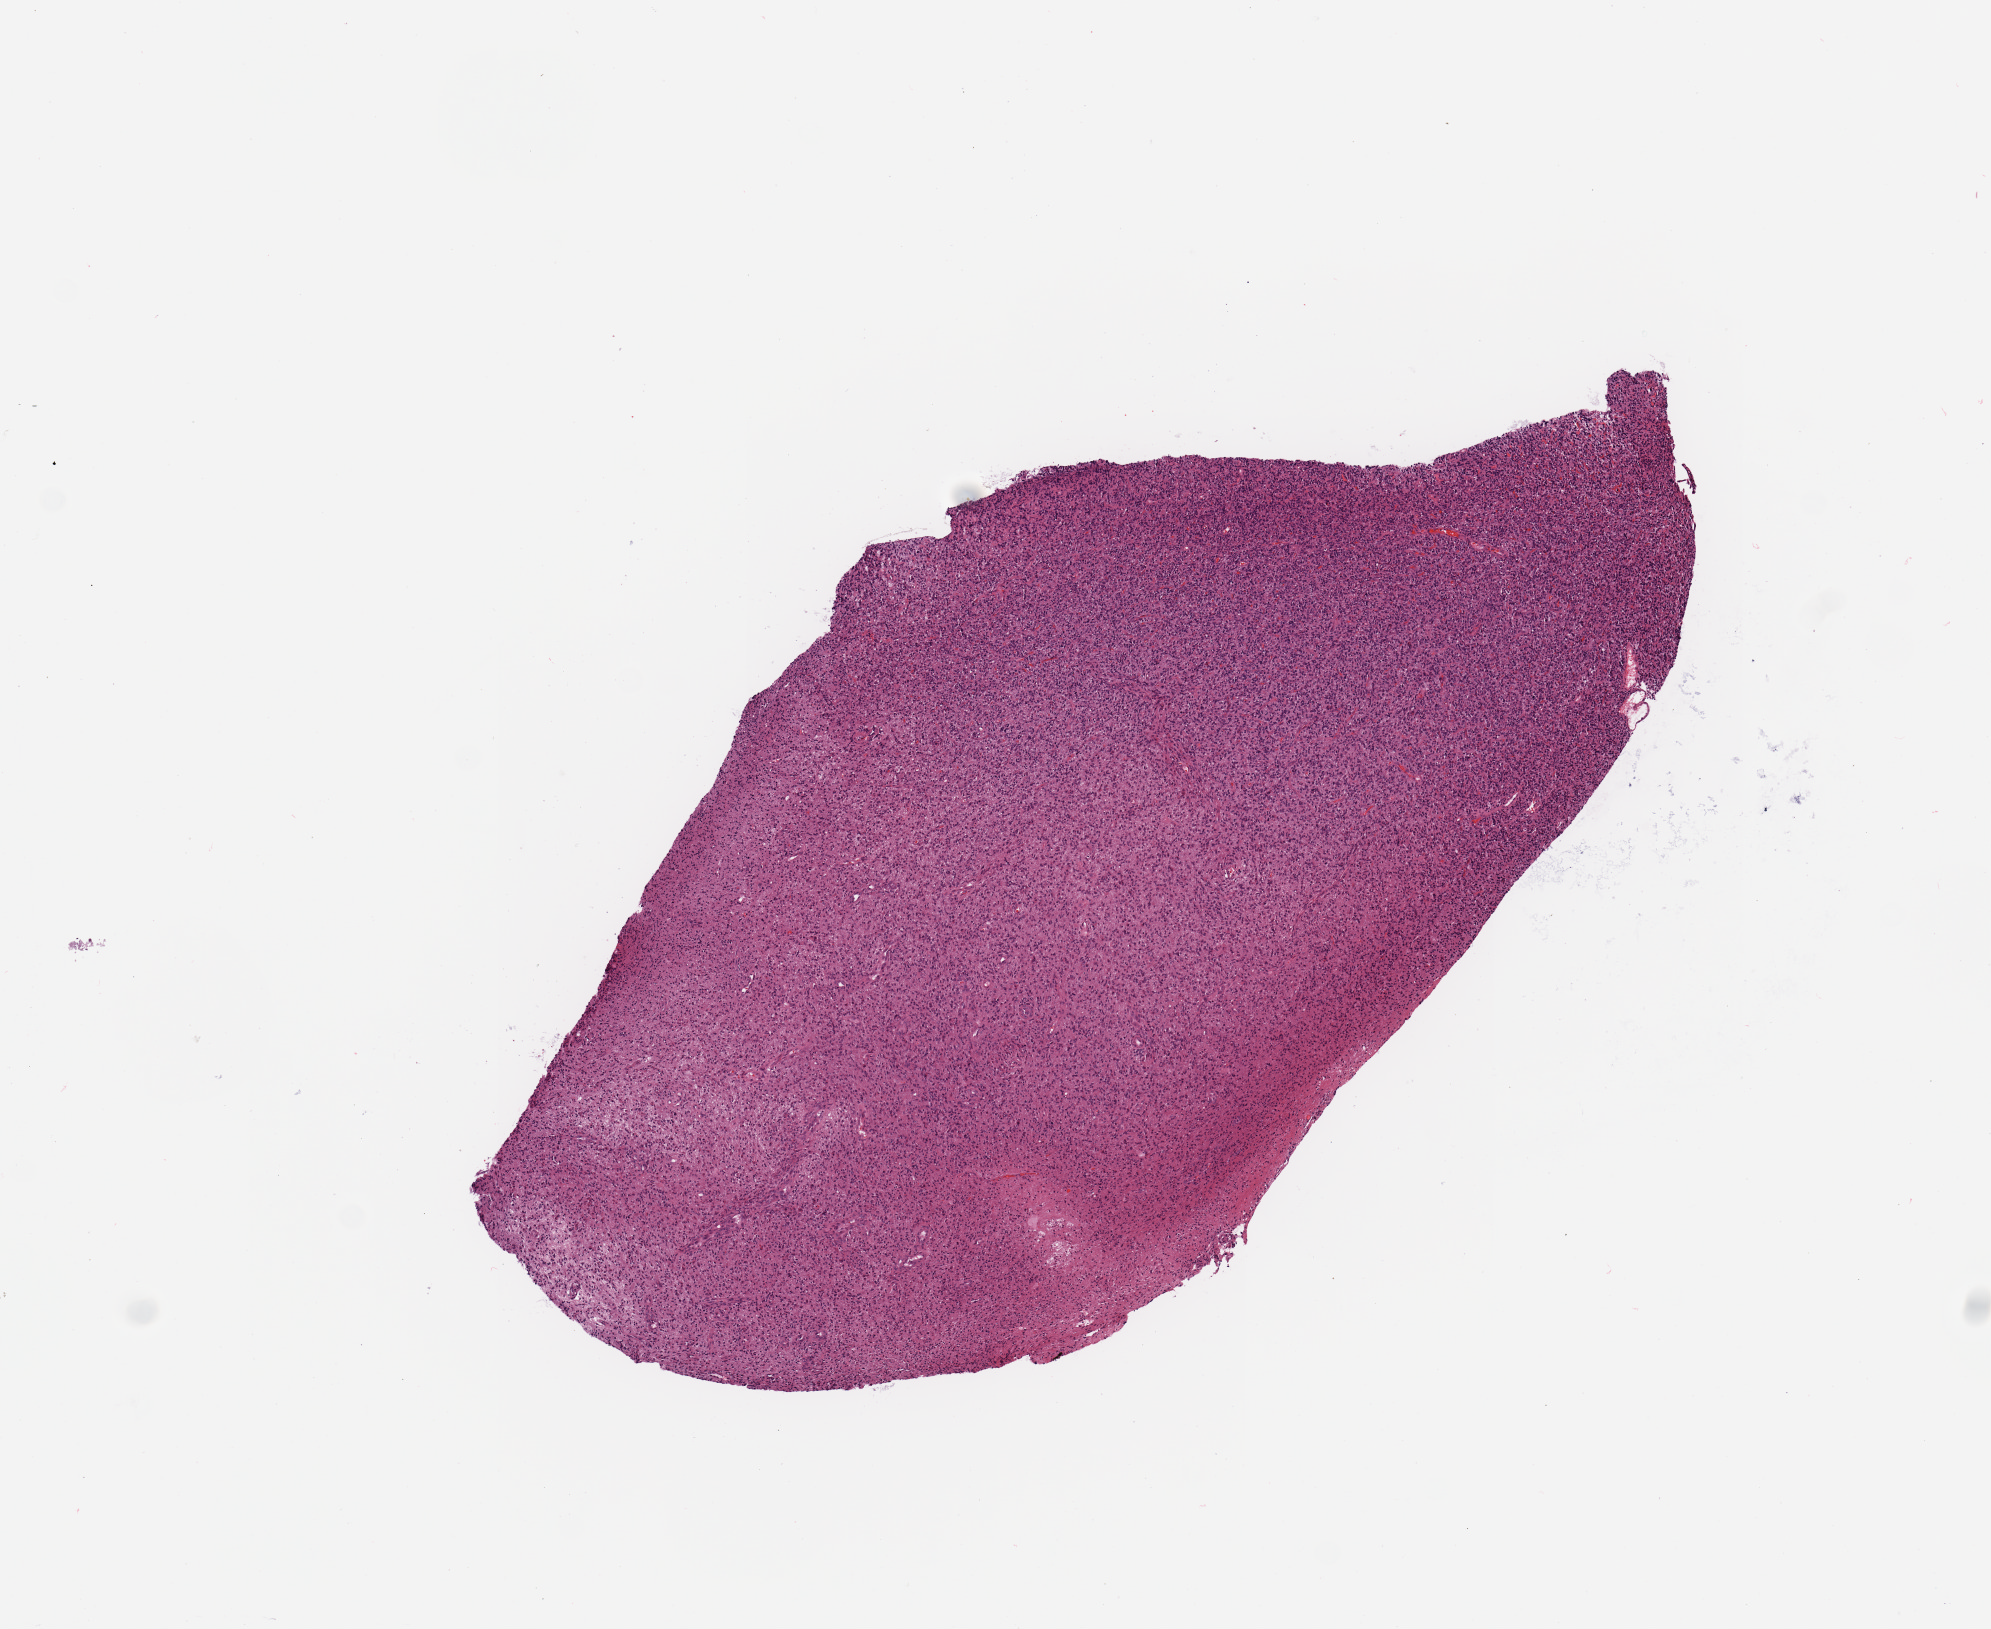
H&E whole-slide image — shown as a low-resolution overview of the whole scanned area (about 7.9 x 6.4 mm); tumour tissue sample, sampled site: brain. 71-year-old female patient. Composition of this section per pathologist review: tumour nuclei 90%, necrosis 2%.
Primary tumour site (as recorded): parietal lobe. Histologic diagnosis: Glioblastoma.